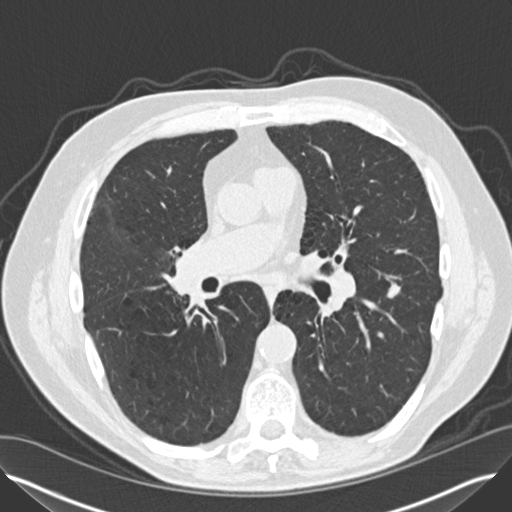
Low-dose screening chest CT, one axial slice. Position 76 of 149 along the scan axis. Lung window (W 1500 / L -600 HU). 2 mm slice thickness. 512 × 512 image matrix, field of view 370 × 370 mm.
Structures marked on this image (manually delineated by an expert):
- lesion 1 (tumor, lower lobe of left lung): box from (x=387, y=283) to (x=401, y=299) px
- lesion 2 (tumor, hilum of right lung): (x=190, y=282)–(x=206, y=303)